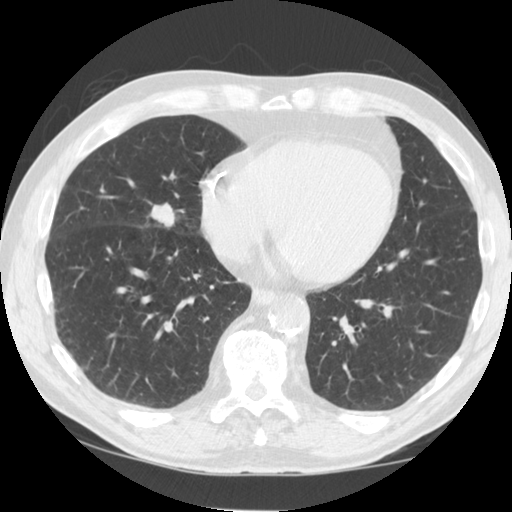
Low-dose screening chest CT, one axial slice. Slice 40 of 125 in the series (ordered by position). 120 kVp. Lung window (W 1500 / L -600 HU). 2.5 mm slice thickness. 512 × 512 image matrix, field of view 350 × 350 mm.
Structures marked on this image (manually delineated by an expert):
- lesion 1 (tumor, middle lobe of right lung): bounding box <151,203,175,227> (left, top, right, bottom; pixels)